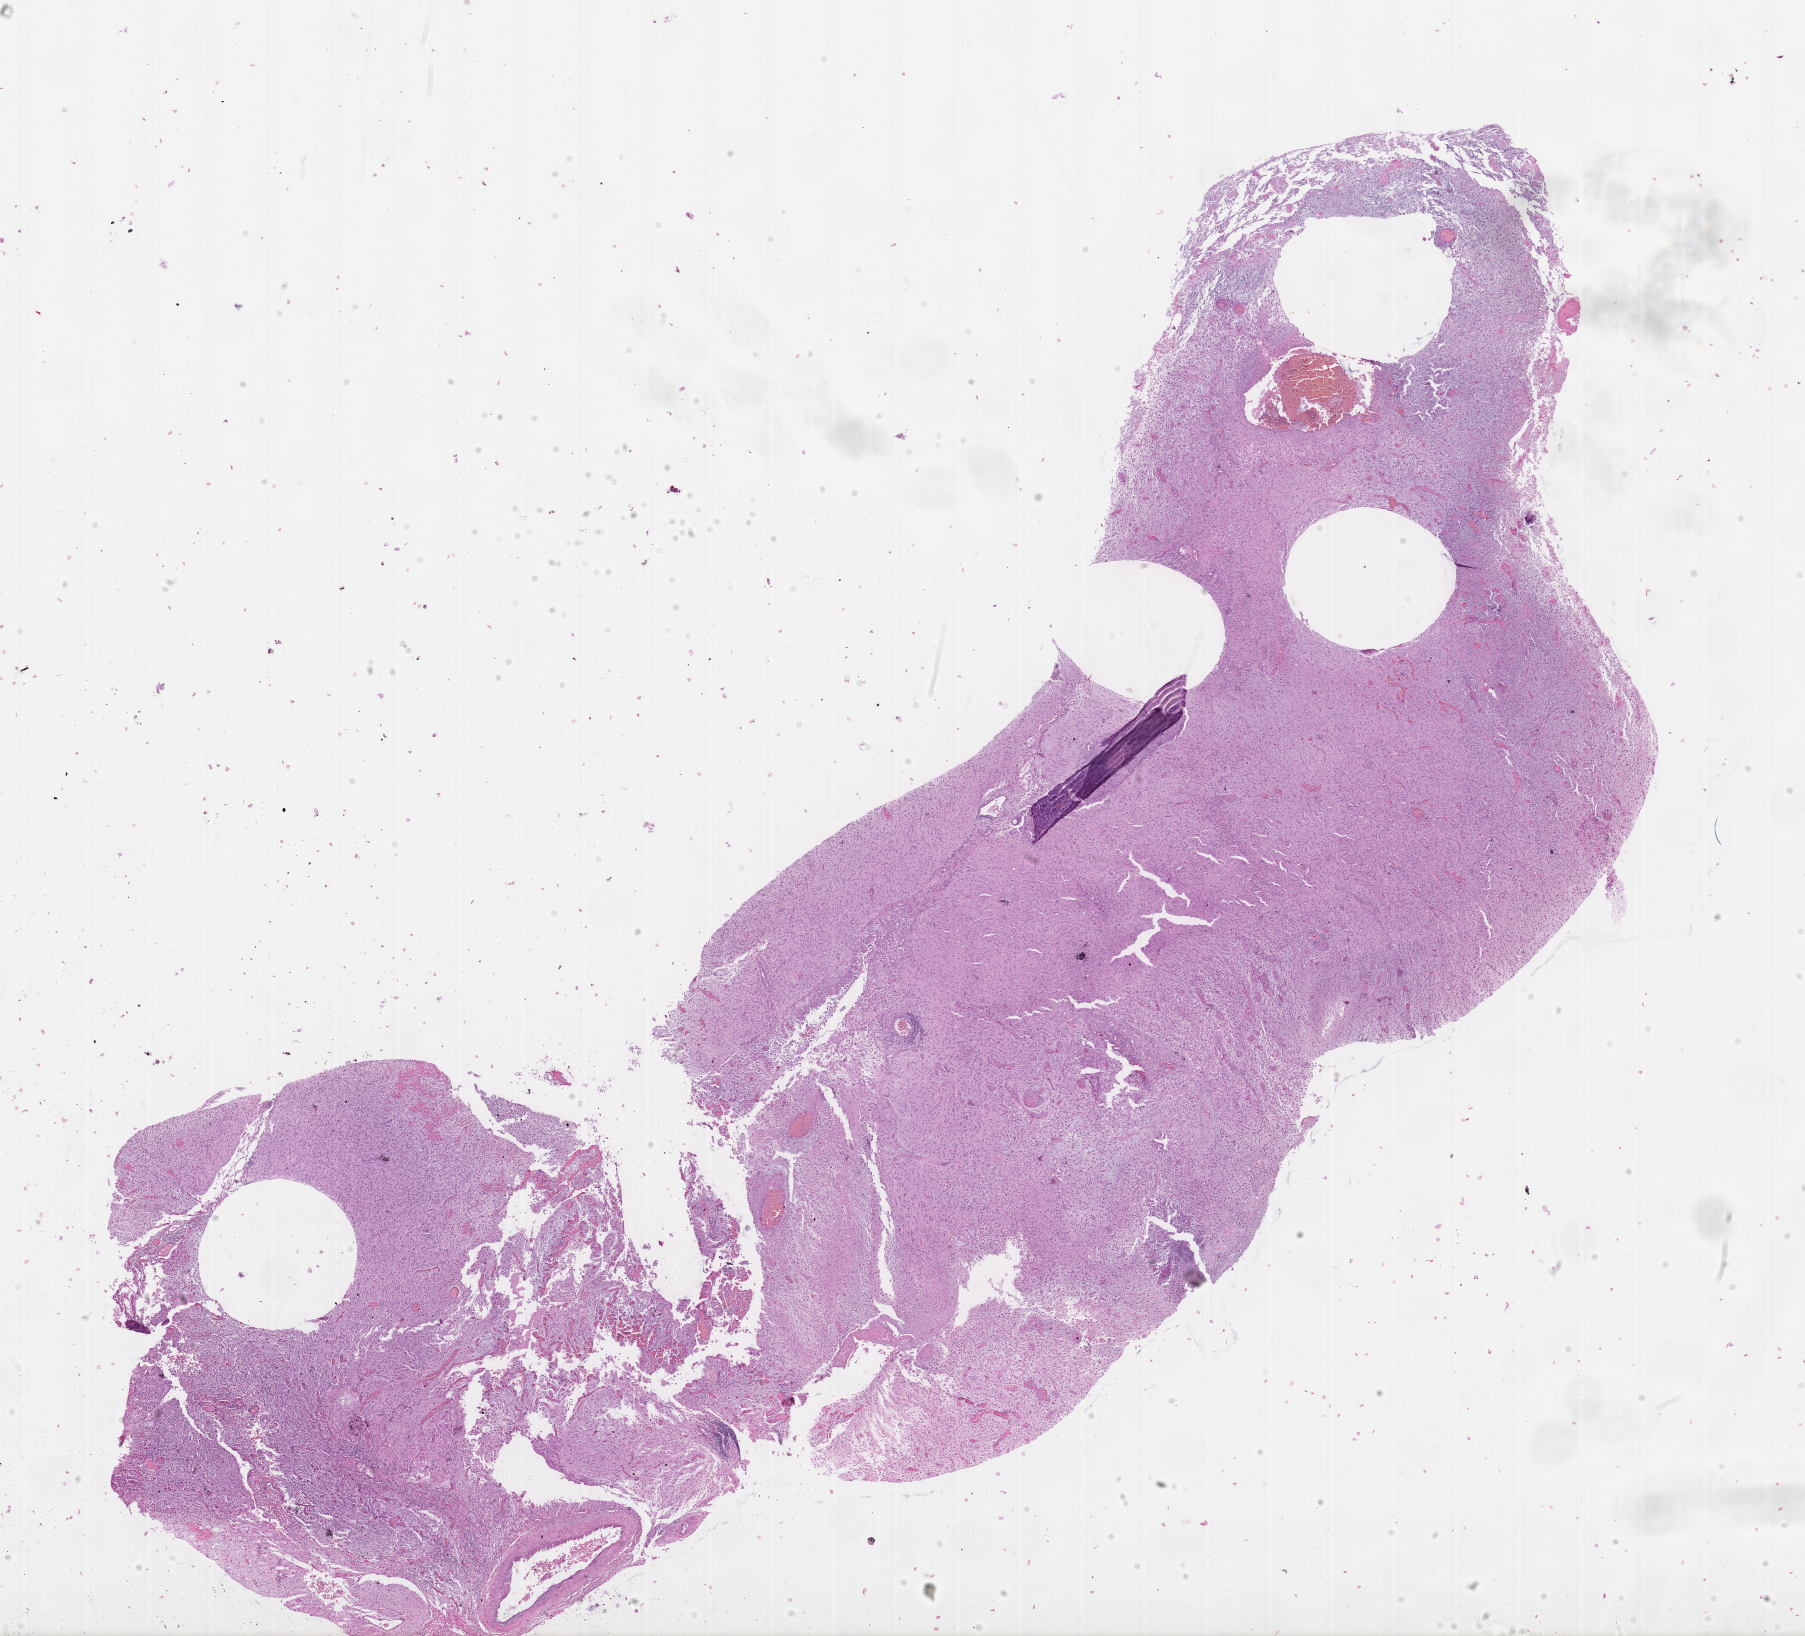
Digitized H&E-stained tissue section (whole slide) — a low-resolution overview of the entire scanned area, about 14.6 x 13.3 mm (from a 40x scan). FFPE section. Sample: primary tumour, brain. Patient: male, age at initial diagnosis 57 years.
- pathologic diagnosis: Glioblastoma